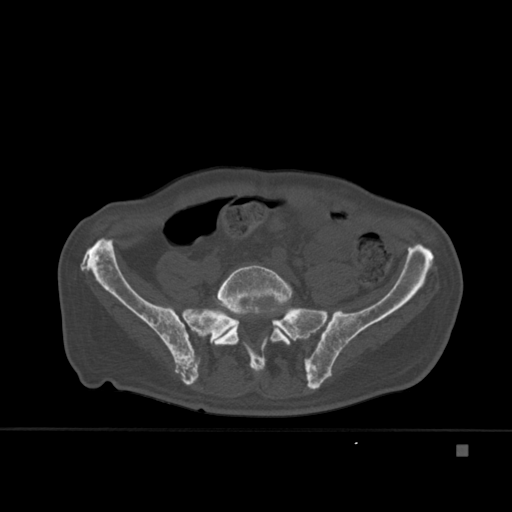
CT including the spine, one axial slice; position 96 of 451 along the scan axis; bone window (W 1800 / L 400 HU); 1.5 mm slice thickness; 512 × 512 image matrix. Male patient, age 75 years. Case-level facts recorded for this patient, not image findings: primary cancer: prostate.
Outlined on this slice (semi-automatically segmented with operator editing):
- L5 vertebra: bounding box (x1, y1, x2, y2) in pixels: (212, 265, 293, 367)